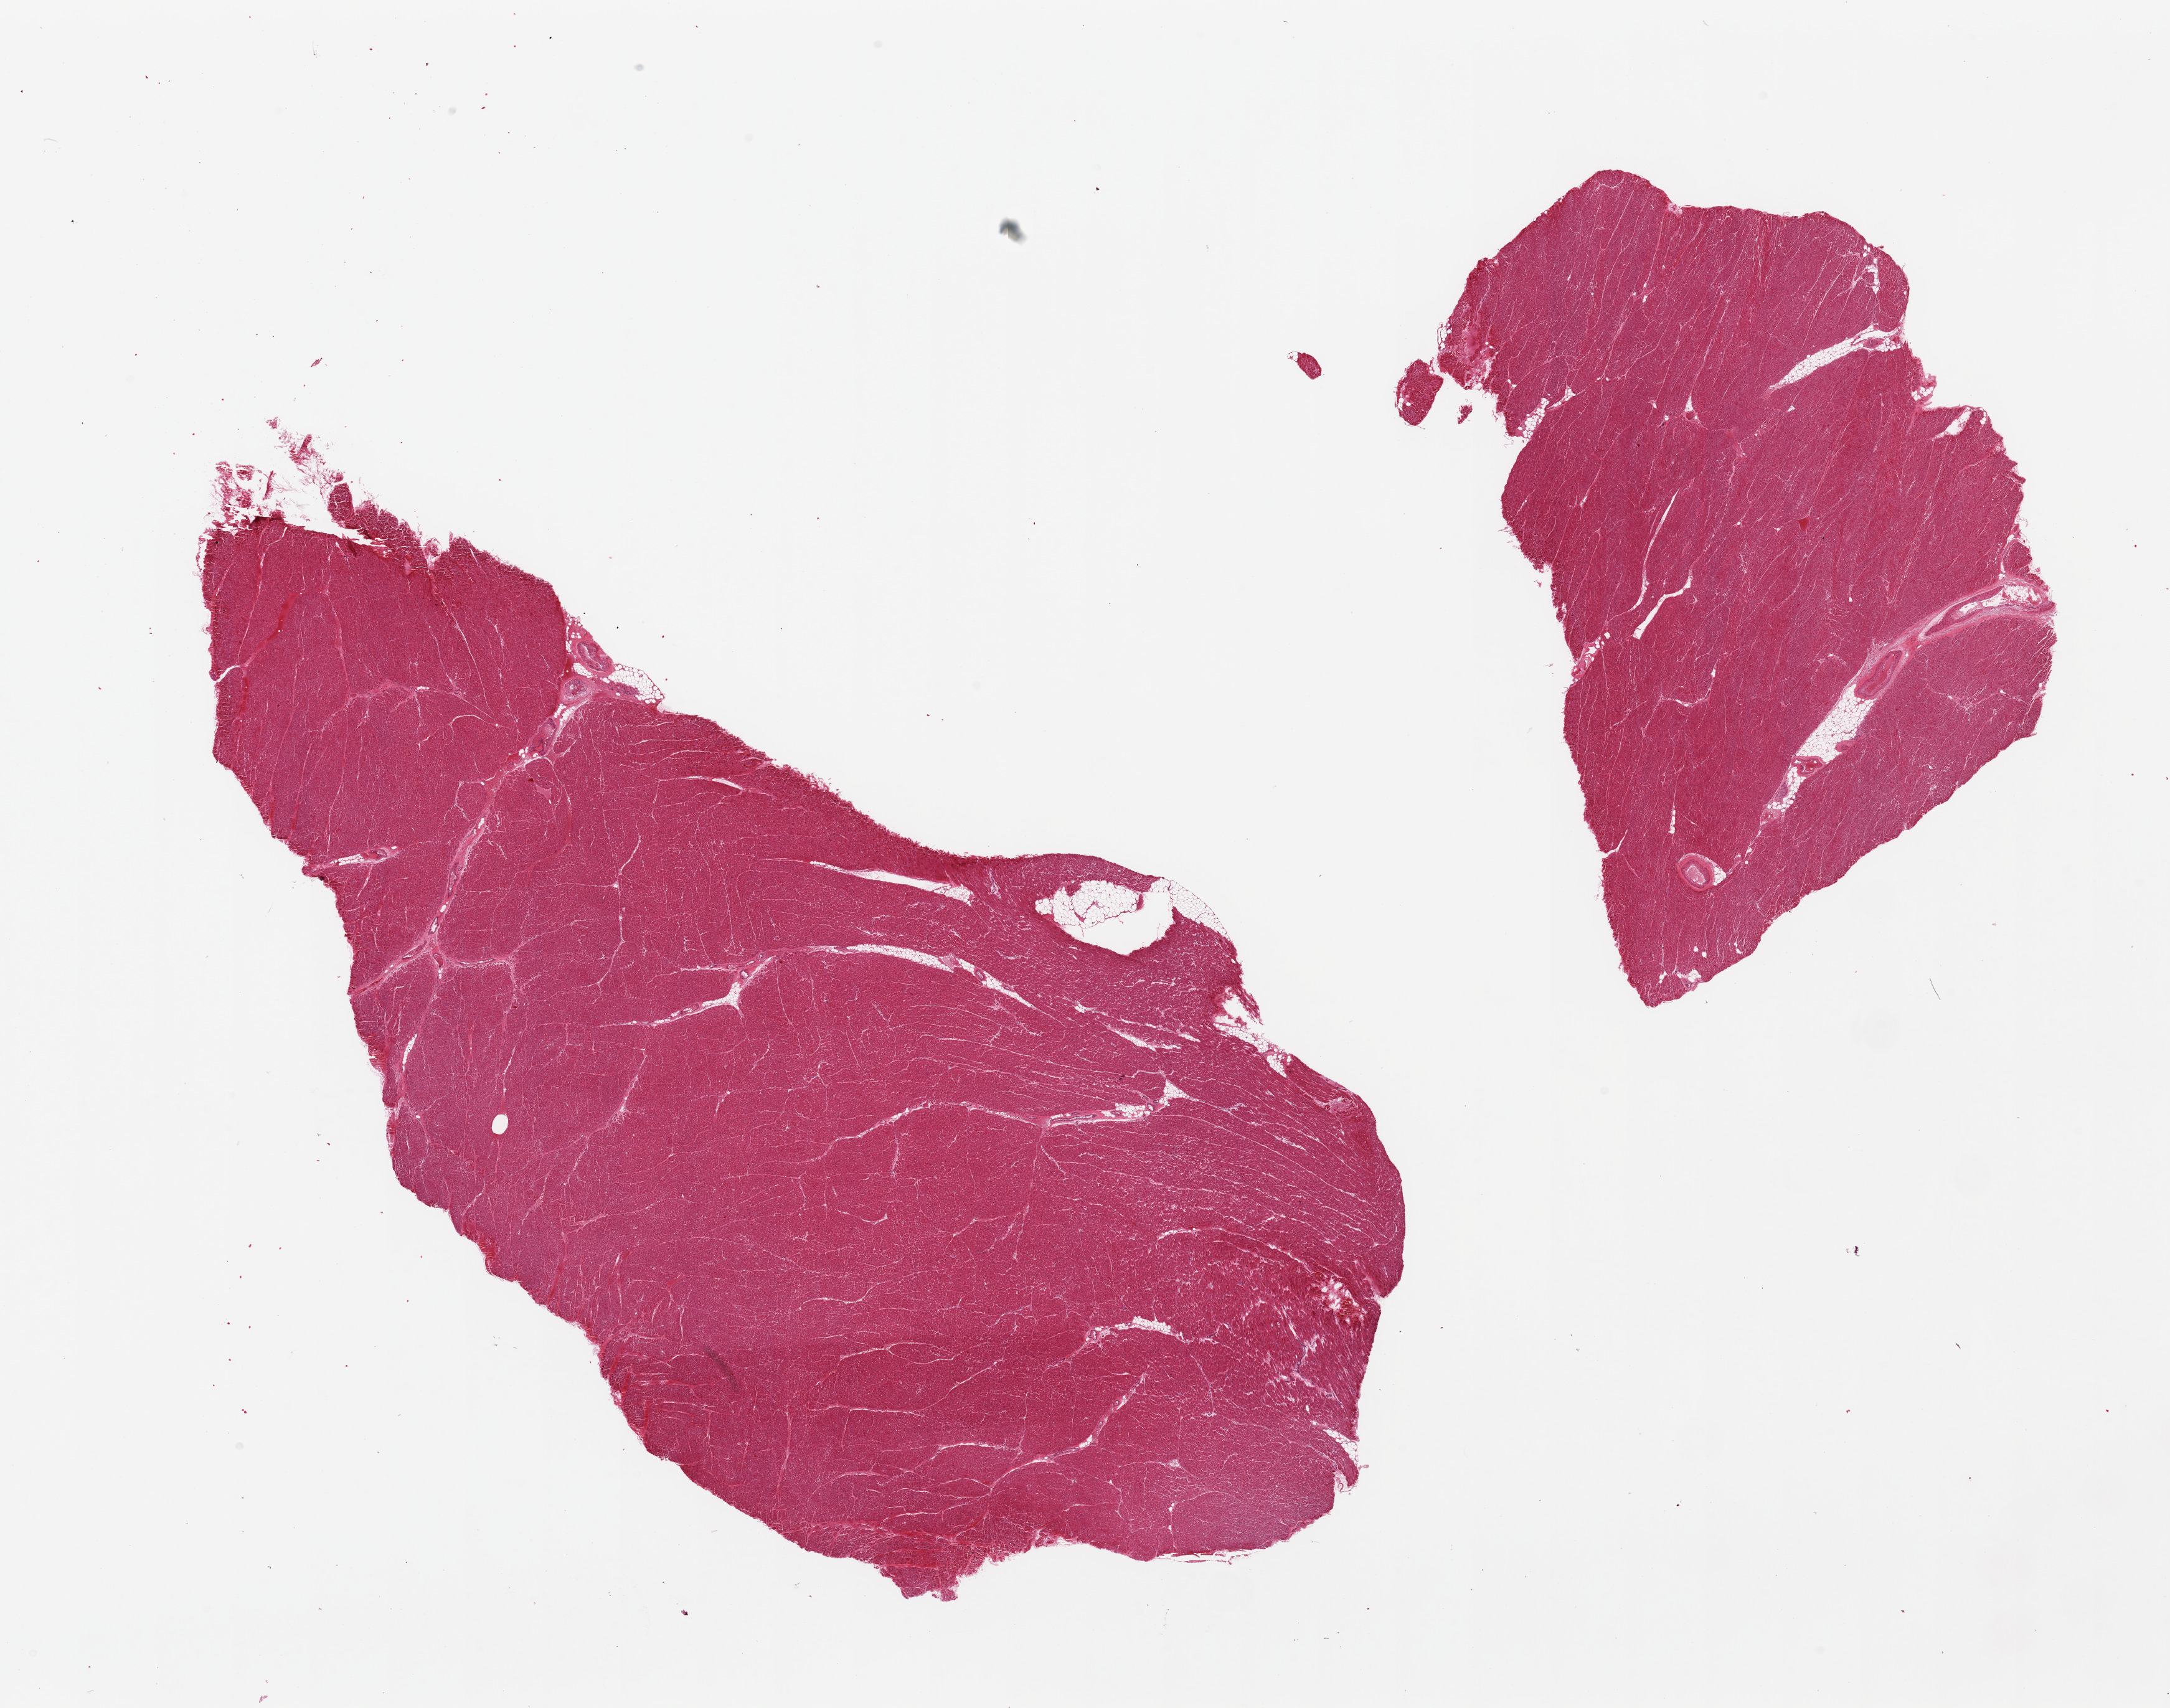
Whole-slide image, hematoxylin and eosin (H&E) stain, low-resolution overview of the scanned area, about 27.6 x 21.7 mm (slide scanned at 20x). PAXgene-fixed paraffin-embedded (PFPE) section. Sampled site (target tissue): heart. Tissue donor sample. Male donor.
Pathologist's review note for this sample: 2 pieces. Heart muscle NOT Atrial appendage.